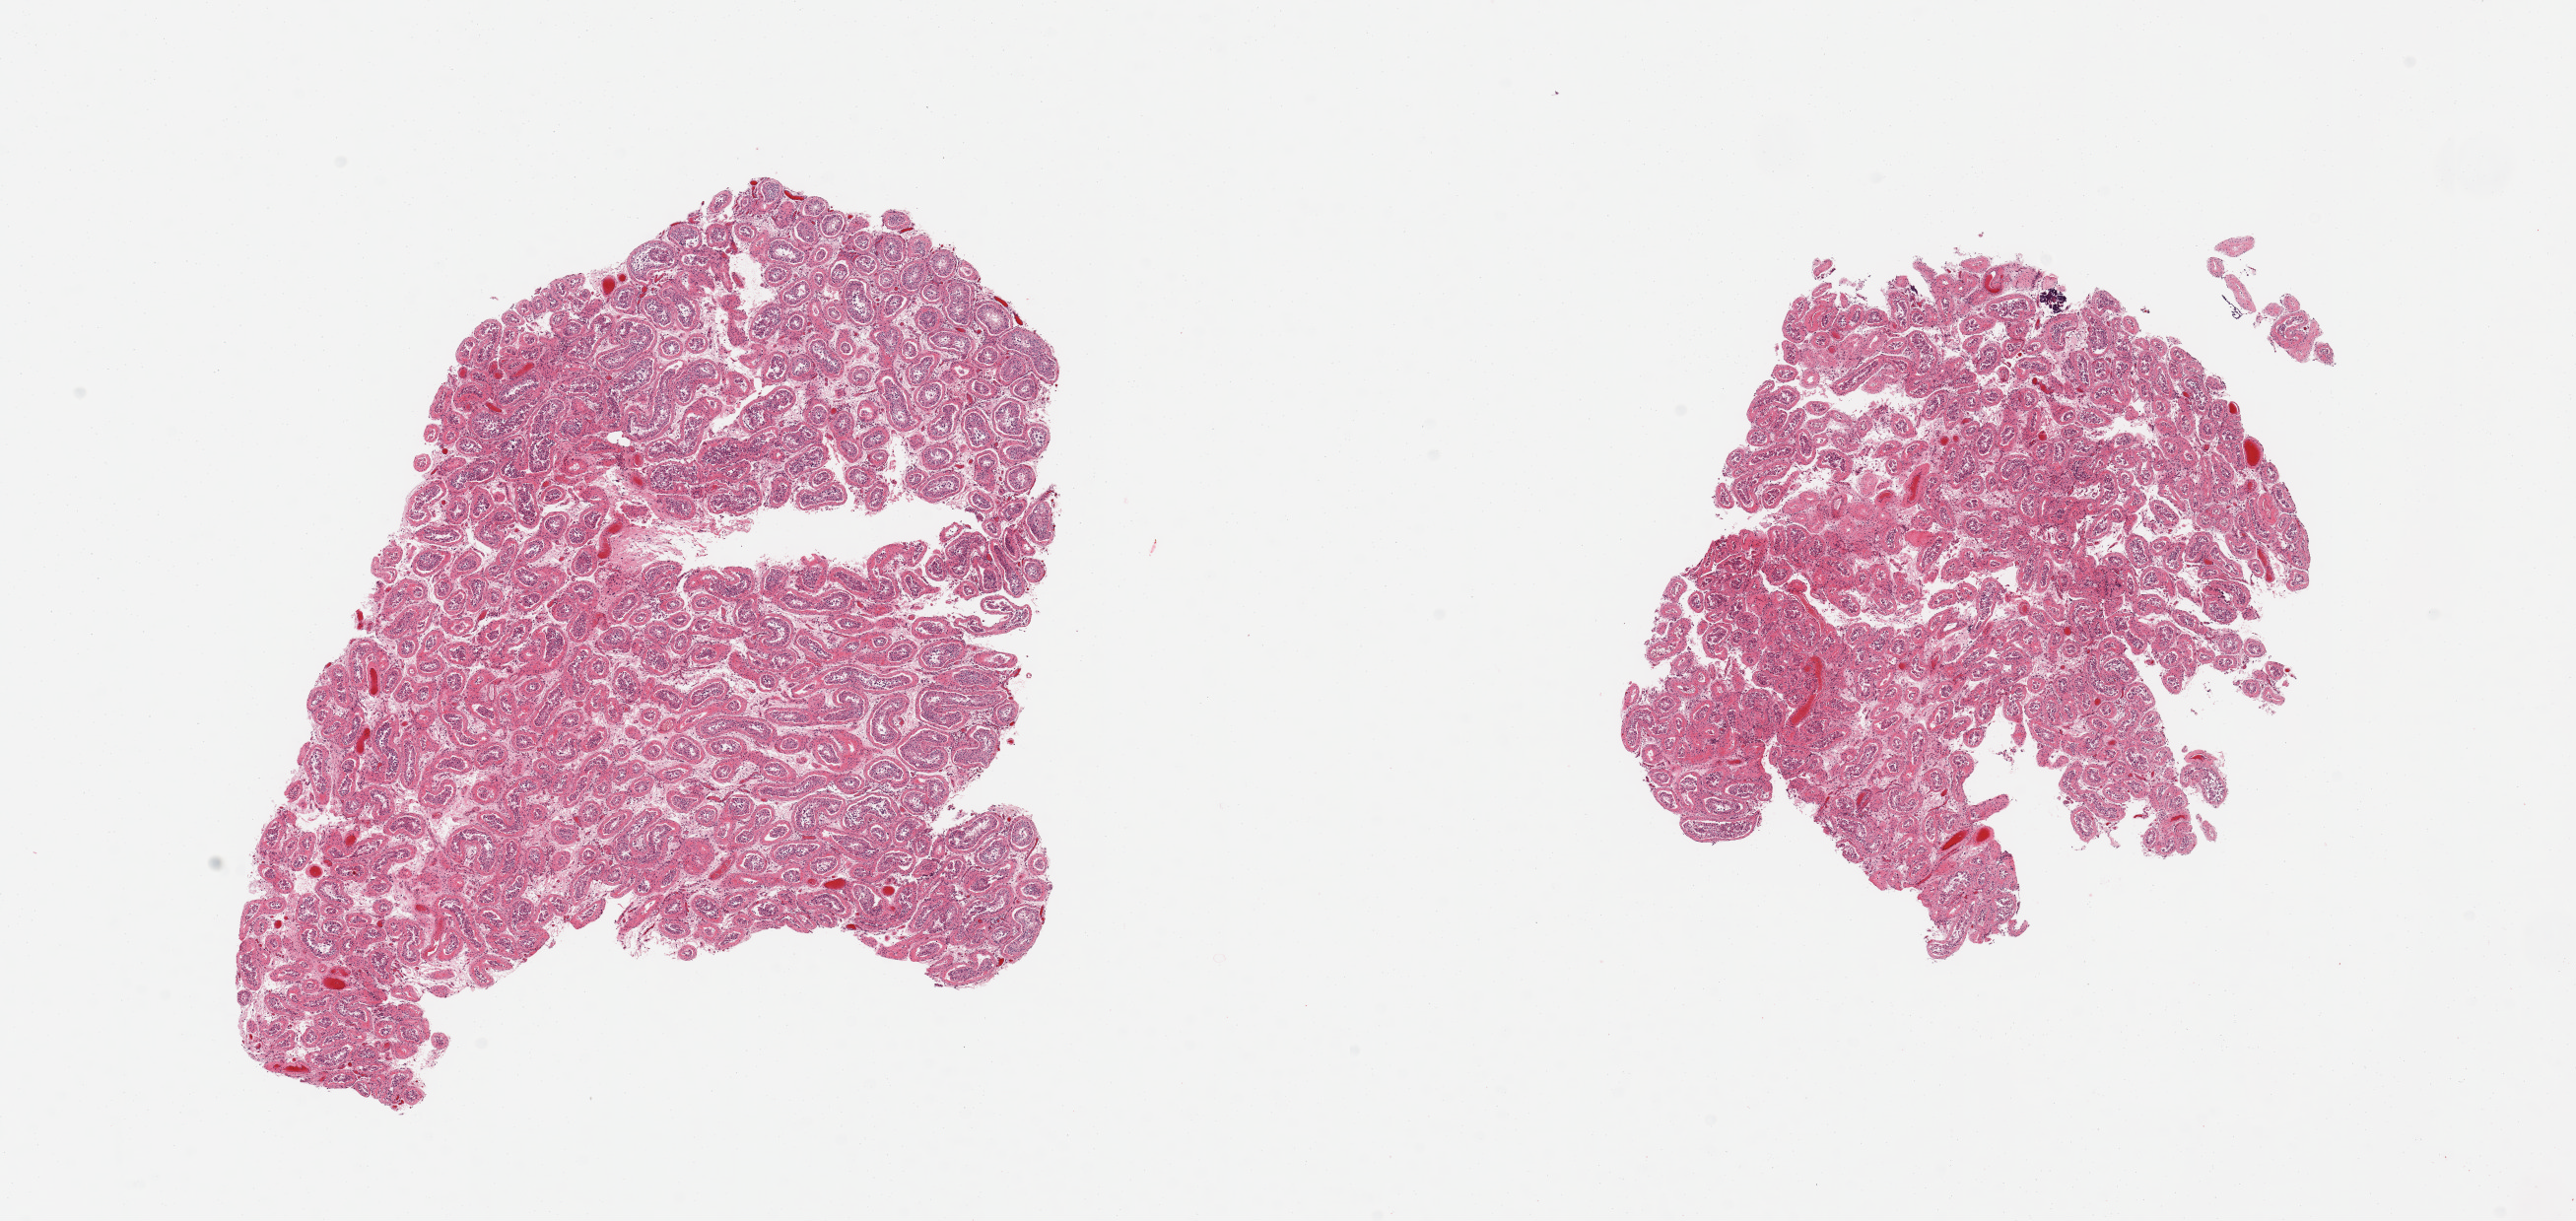
Whole-slide image, H&E stain — whole scanned area (about 20.7 x 9.8 mm) shown as a low-resolution overview. PAXgene-fixed paraffin-embedded (PFPE) section. Sampled site (target tissue): testis. Donor tissue sample. Male donor.
Pathologist's review note for this sample: 2 pieces; increased peritubular fibrosis, reduced/absent spermatogenesis.